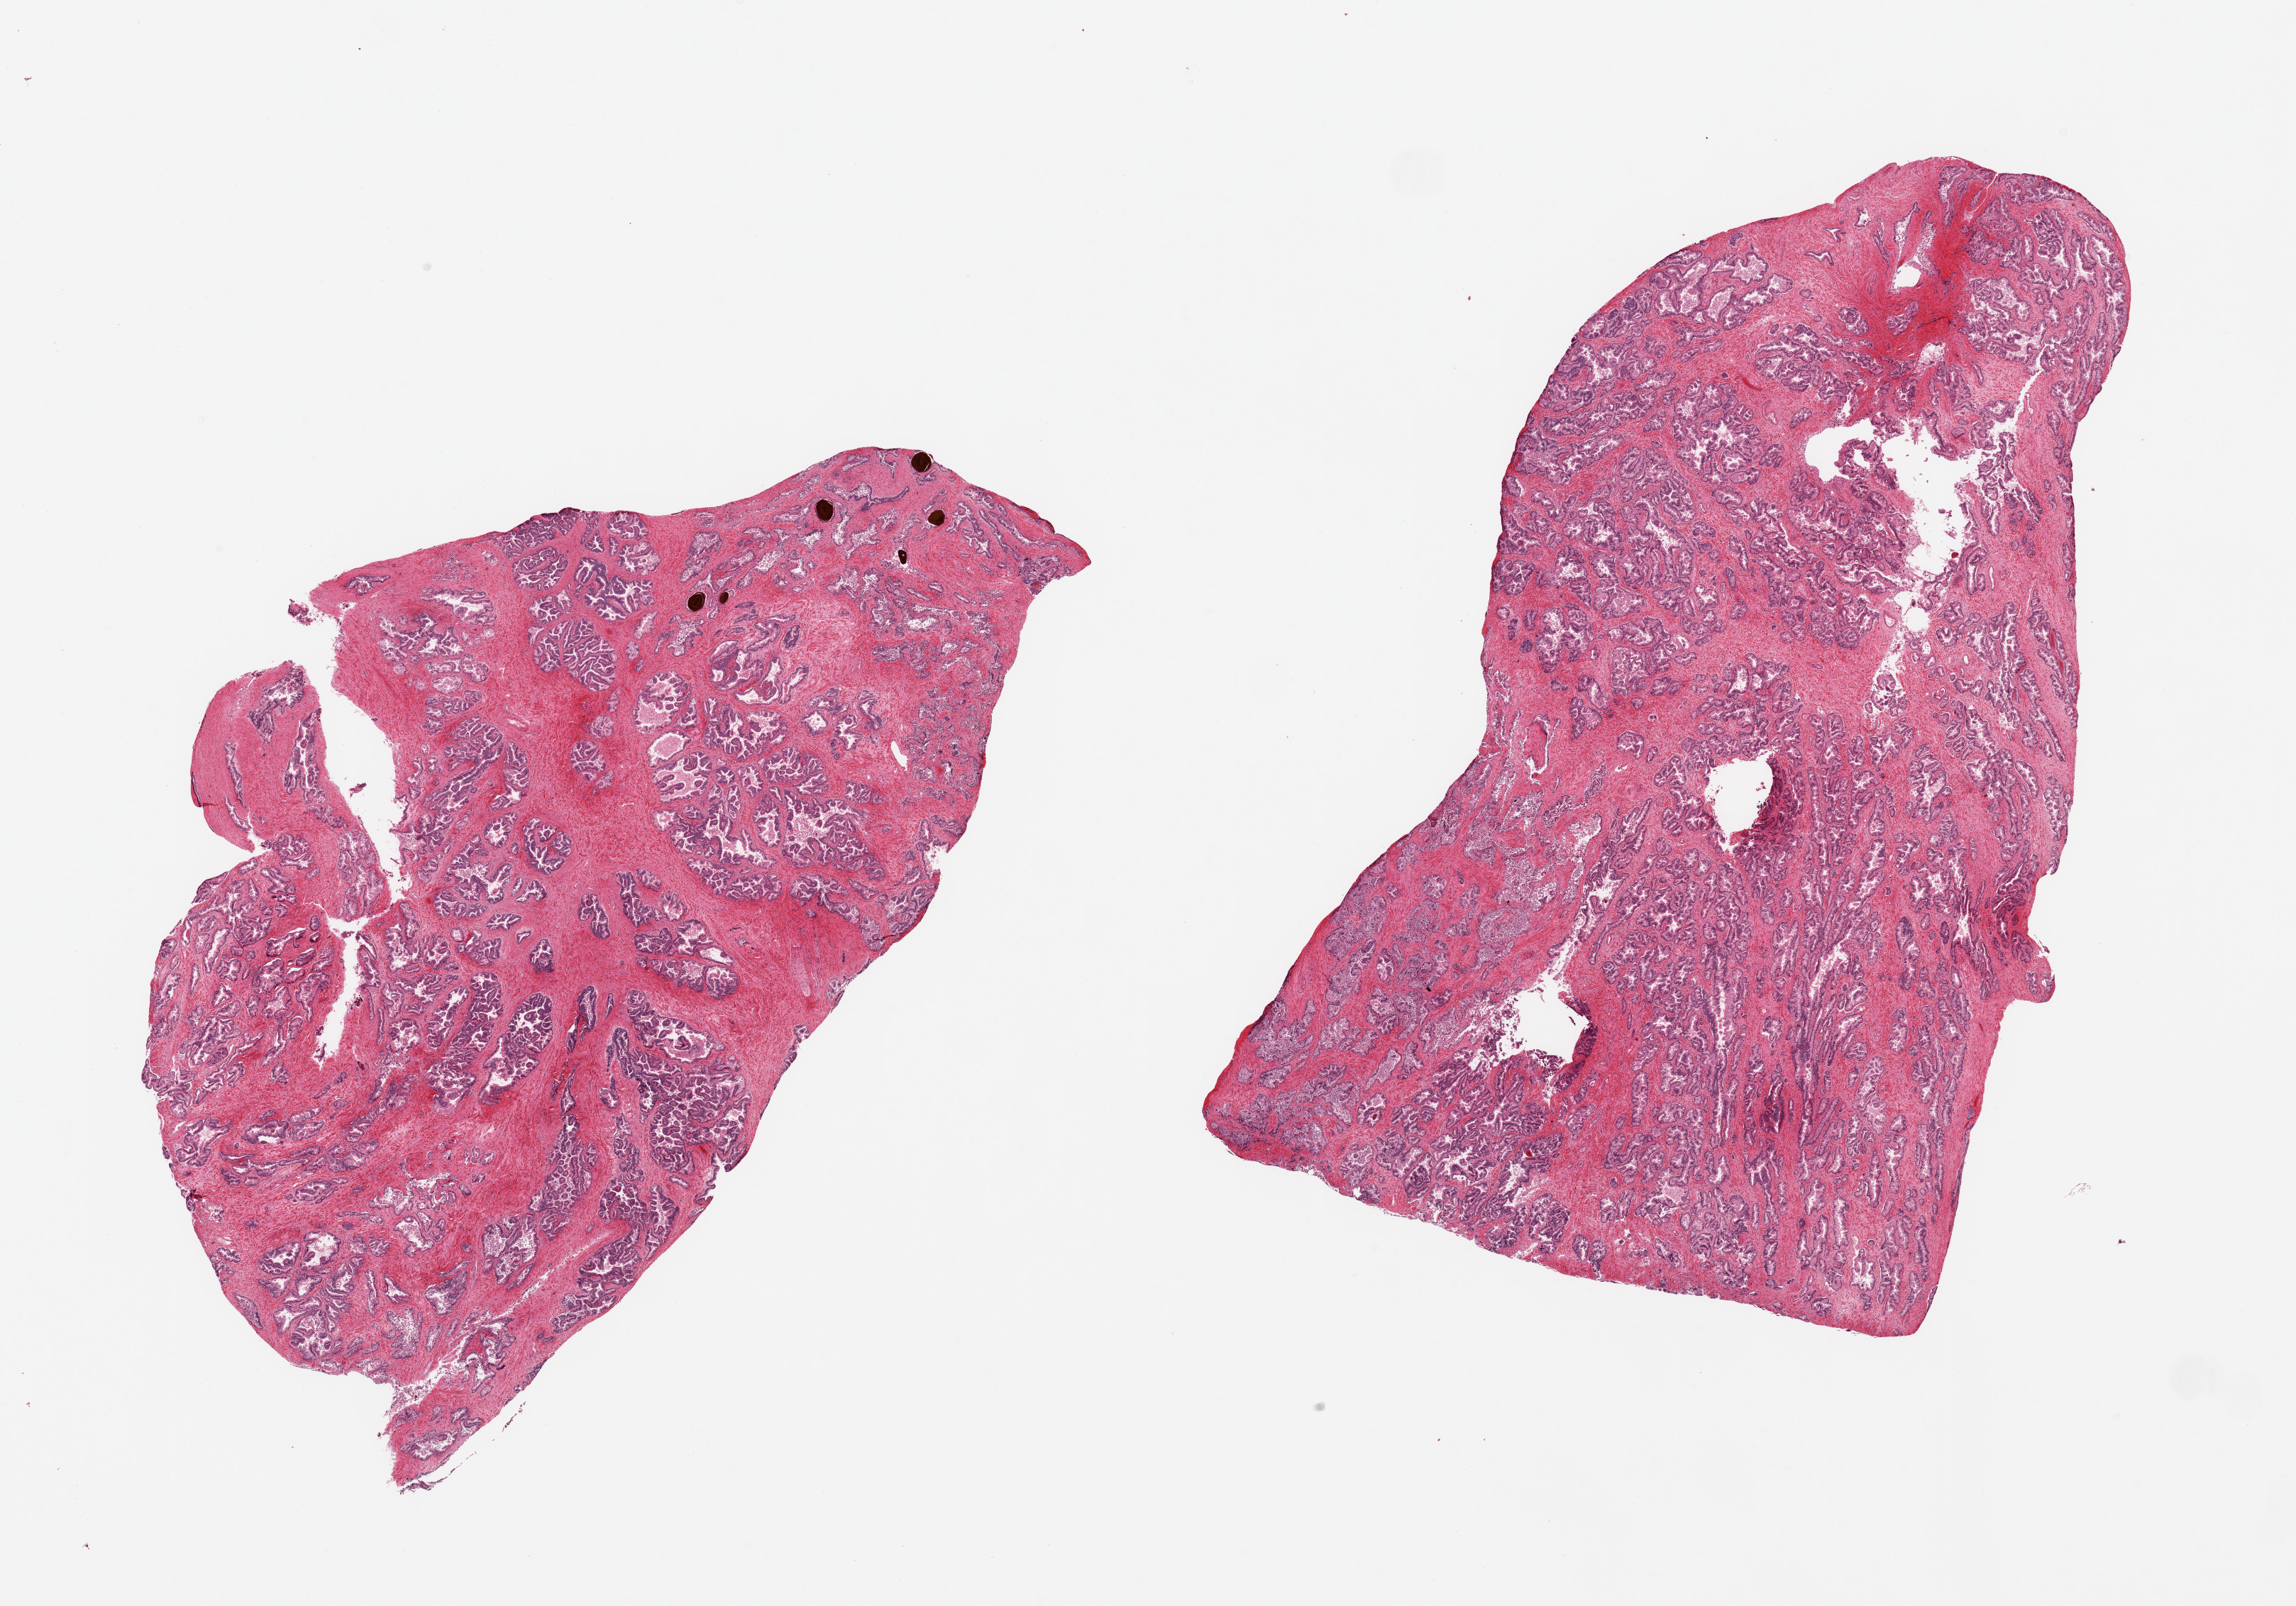
Digitized H&E-stained section, shown as a low-resolution overview of the whole scanned area (about 25.6 x 17.9 mm, acquisition: 20x scan); PAXgene-fixed paraffin-embedded (PFPE) section; sampled site (target tissue): prostate; donor tissue sample. Male donor.
Review note (as recorded): 2 pieces; some glands are moderately autolyzed.